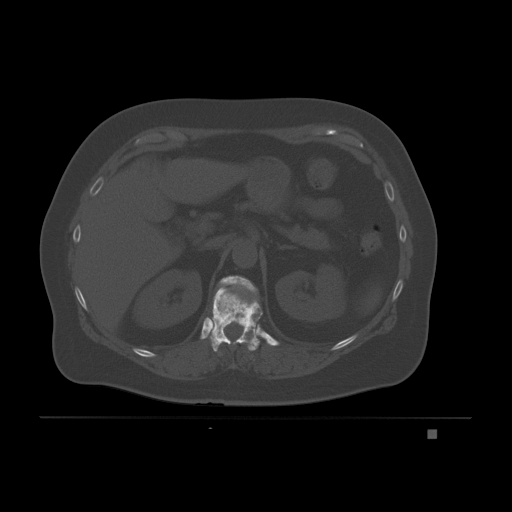
CT including the spine, one axial slice; slice 90 of 221 in the series (ordered by position); bone window (W 1800 / L 400 HU); 3 mm slice thickness; 512 × 512 image matrix, field of view 474 × 474 mm. Patient: female, 63 years. From the clinical record (not read from this slice): primary cancer: breast.
Structures marked on this image (semi-automatic segmentation, software-assisted and operator-edited):
- T11 vertebra: bounding box [x1, y1, x2, y2] px = [209, 288, 263, 352]
- T12 vertebra: [219, 276, 257, 295]